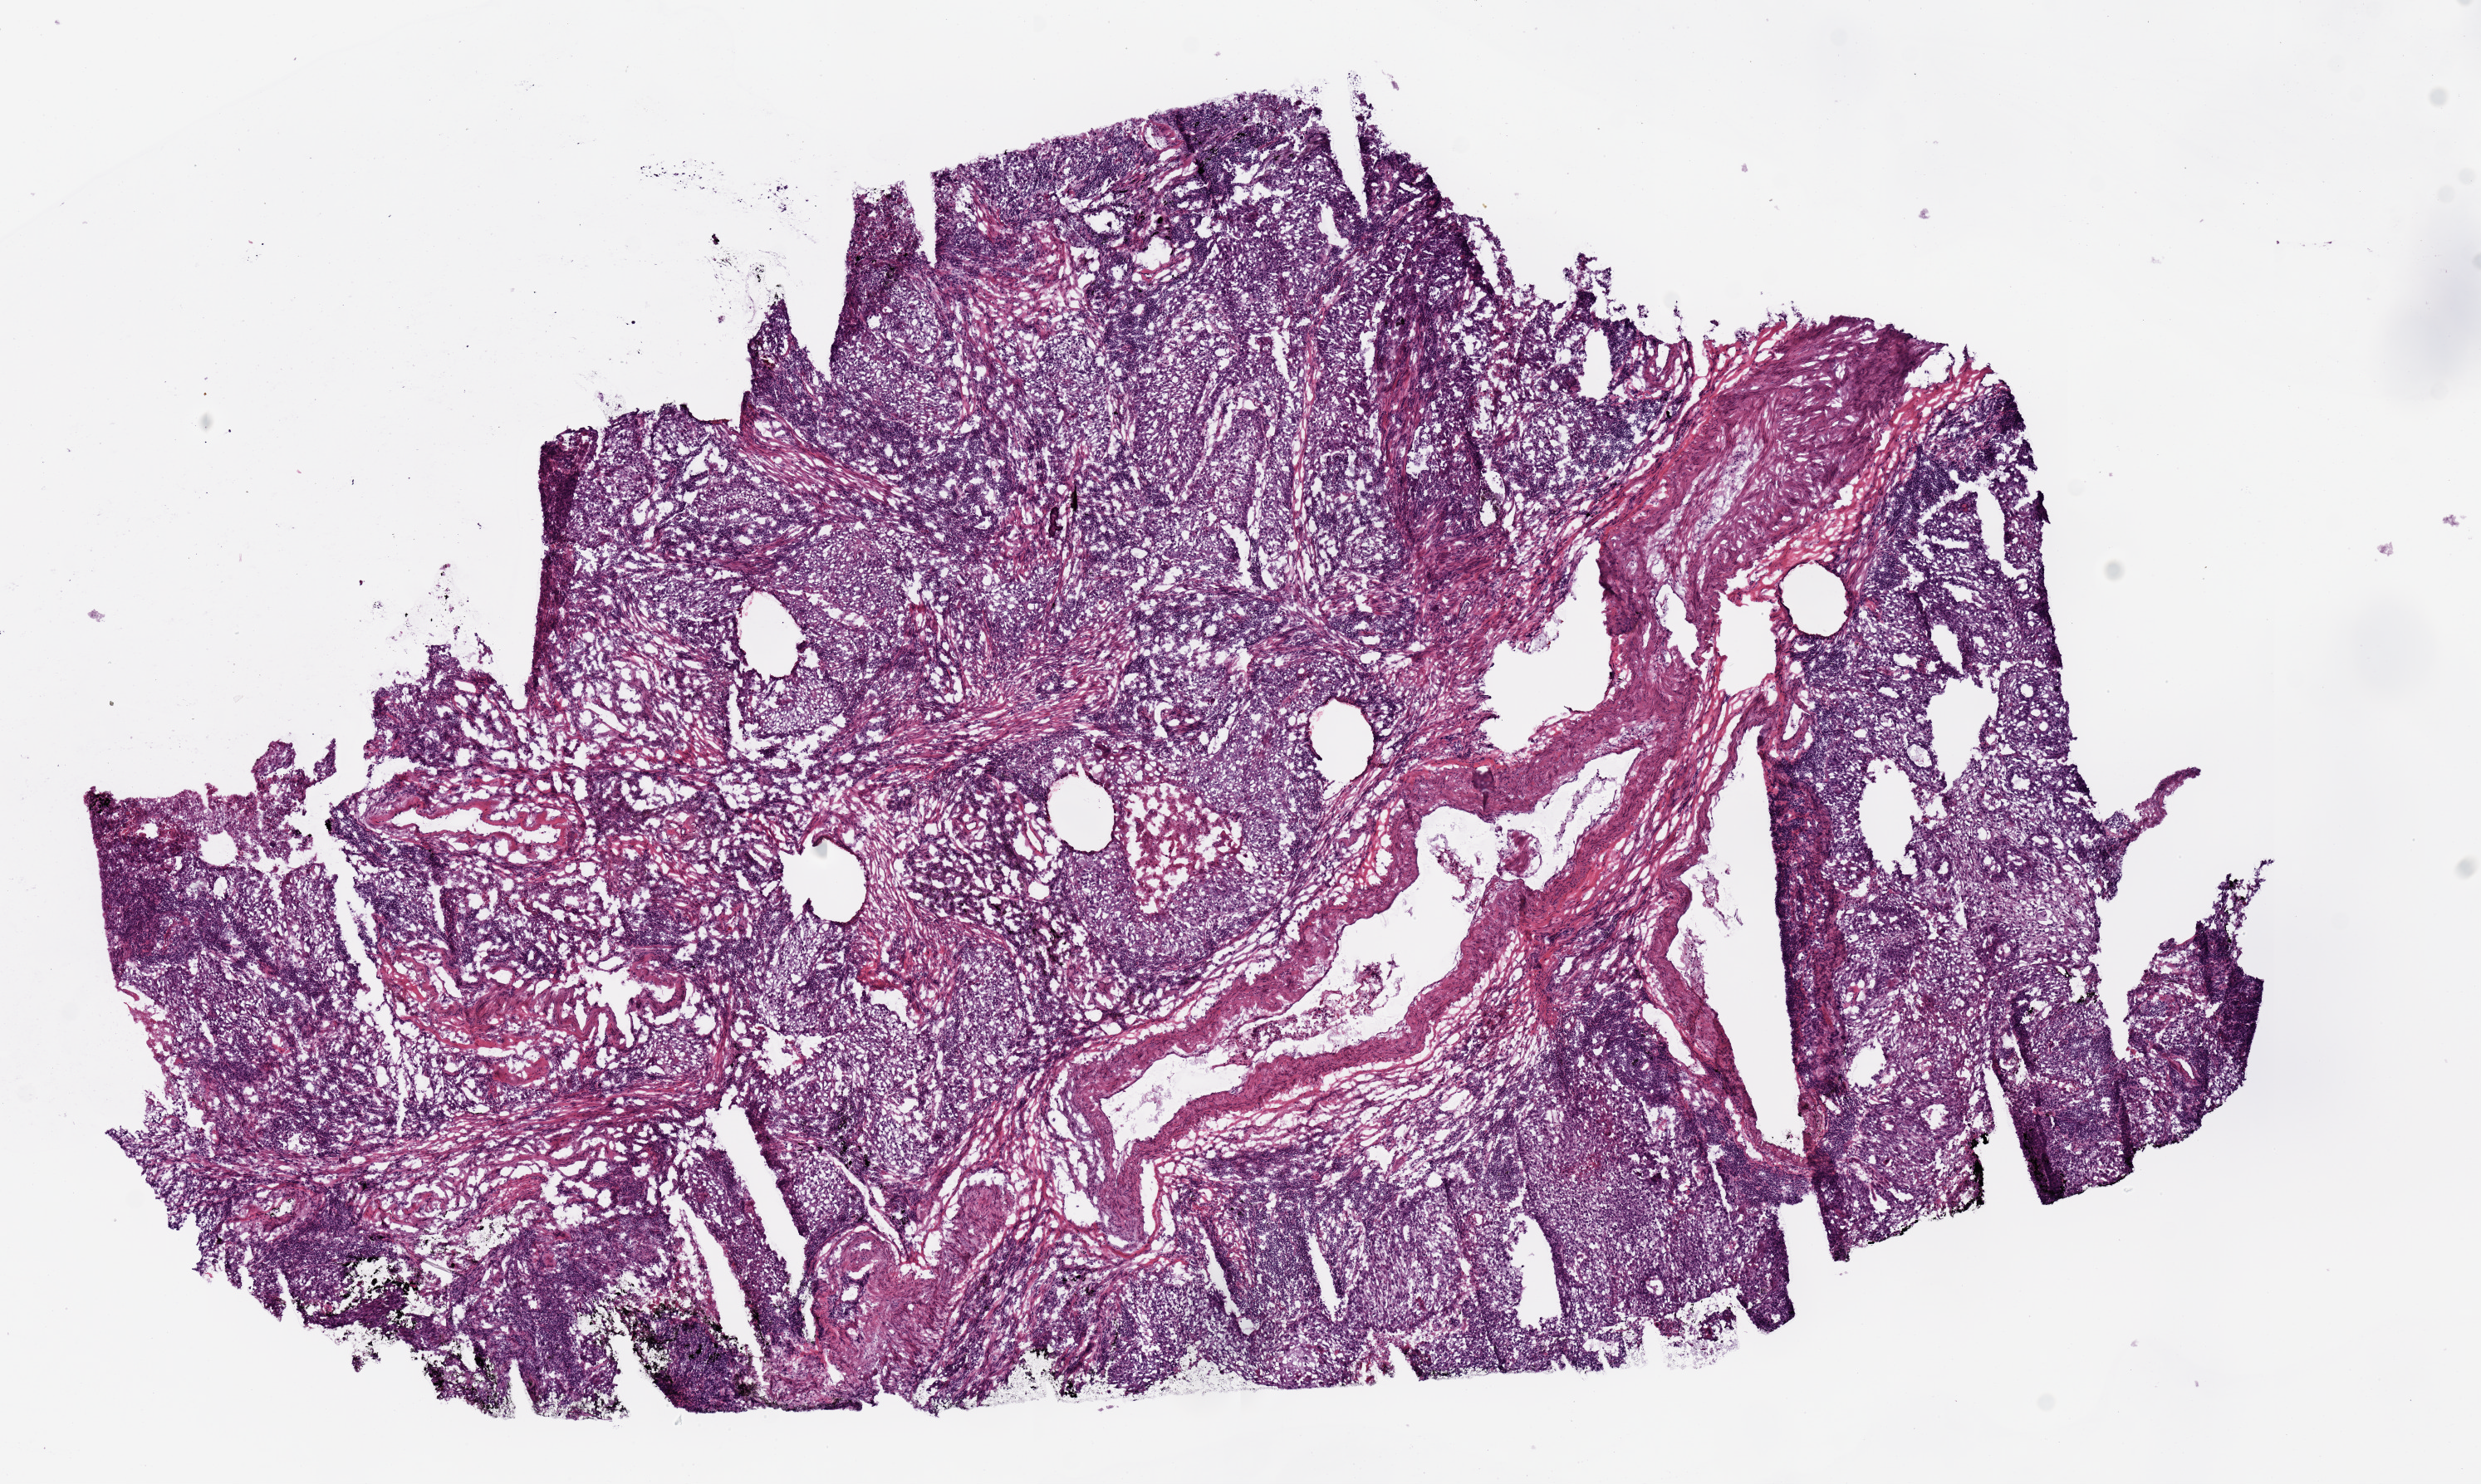
Whole-slide histology image, H&E — shown as a low-resolution overview of the whole scanned area (about 11.8 x 7.1 mm, acquisition: 20x scan); frozen section from the top of the tissue portion; primary tumour sample from the lung. Female, age 73 years at initial diagnosis. Pathologist review of this section (percent, as recorded): tumour cells 80%, tumour nuclei 65%, normal cells 0%, stromal cells 10%, necrosis 10%.
AJCC pathologic stage: IA (7th edition). Laterality: right. Pathologic diagnosis: Squamous cell carcinoma, NOS (upper lobe, lung). TNM: T1b N0 MX.